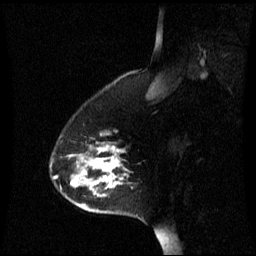
Breast MRI (dynamic contrast-enhanced), one sagittal slice; slice 15 of 60 in the series (ordered by position); dynamic contrast-enhanced series, image 2 of 3 at this slice position (ordered by acquisition); 1.5 T; TE 4.2 ms, TR 8.4 ms; 2.2 mm slice thickness; 256 × 256 image matrix, field of view 240 × 240 mm. Female patient, age 45 years. Case-level facts recorded for this patient, not image findings: setting: breast cancer imaged before/during neoadjuvant chemotherapy; receptor status: HR-positive, HER2-negative.
Annotated regions visible in this slice (semi-automatic segmentation, software-assisted and operator-edited):
- analysis volume of interest (the breast-tissue region the enhancement analysis was run in; not a lesion): bounding box <50,134,129,215> (left, top, right, bottom; pixels)
- tumour enhancement mask (voxels above the 70 % enhancement threshold inside the analysis volume of interest): <72,146,121,191>